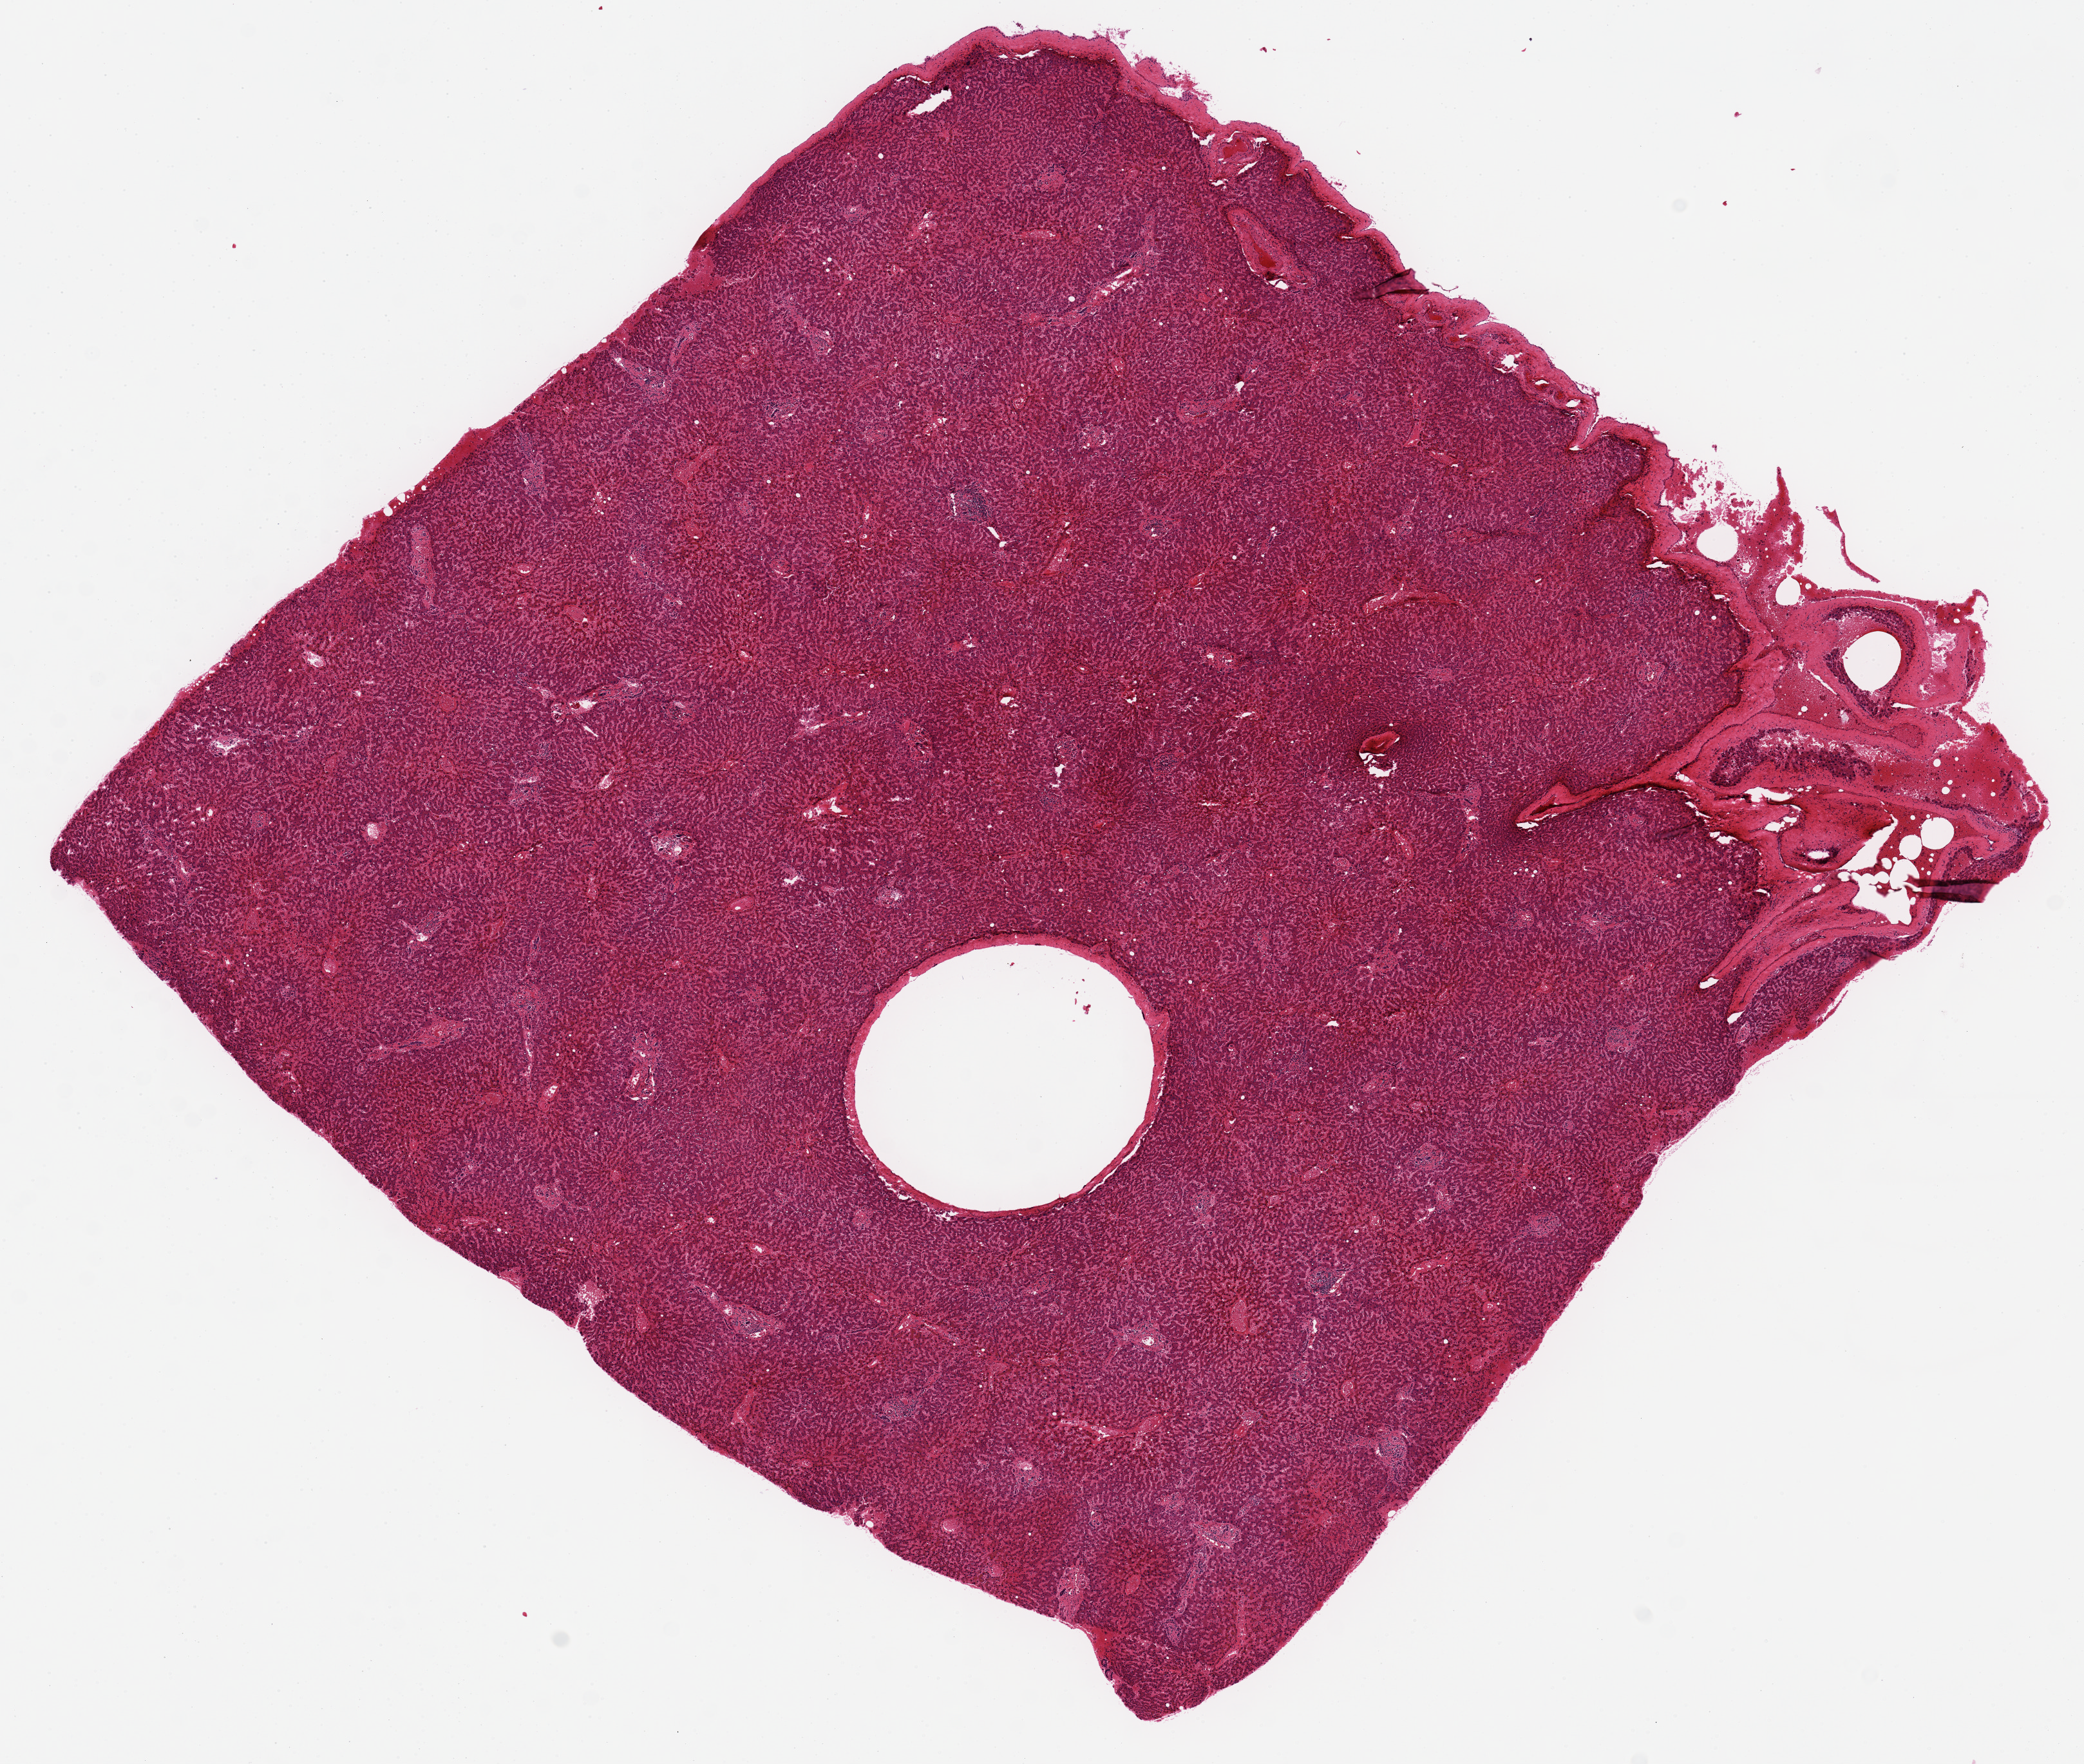
H&E whole-slide image, a low-resolution overview of the entire scanned area, about 12.8 x 10.8 mm, PAXgene-fixed, paraffin-embedded tissue, section of liver (target tissue), donor tissue sample.
Reviewer comment on this tissue sample: mild congestion.